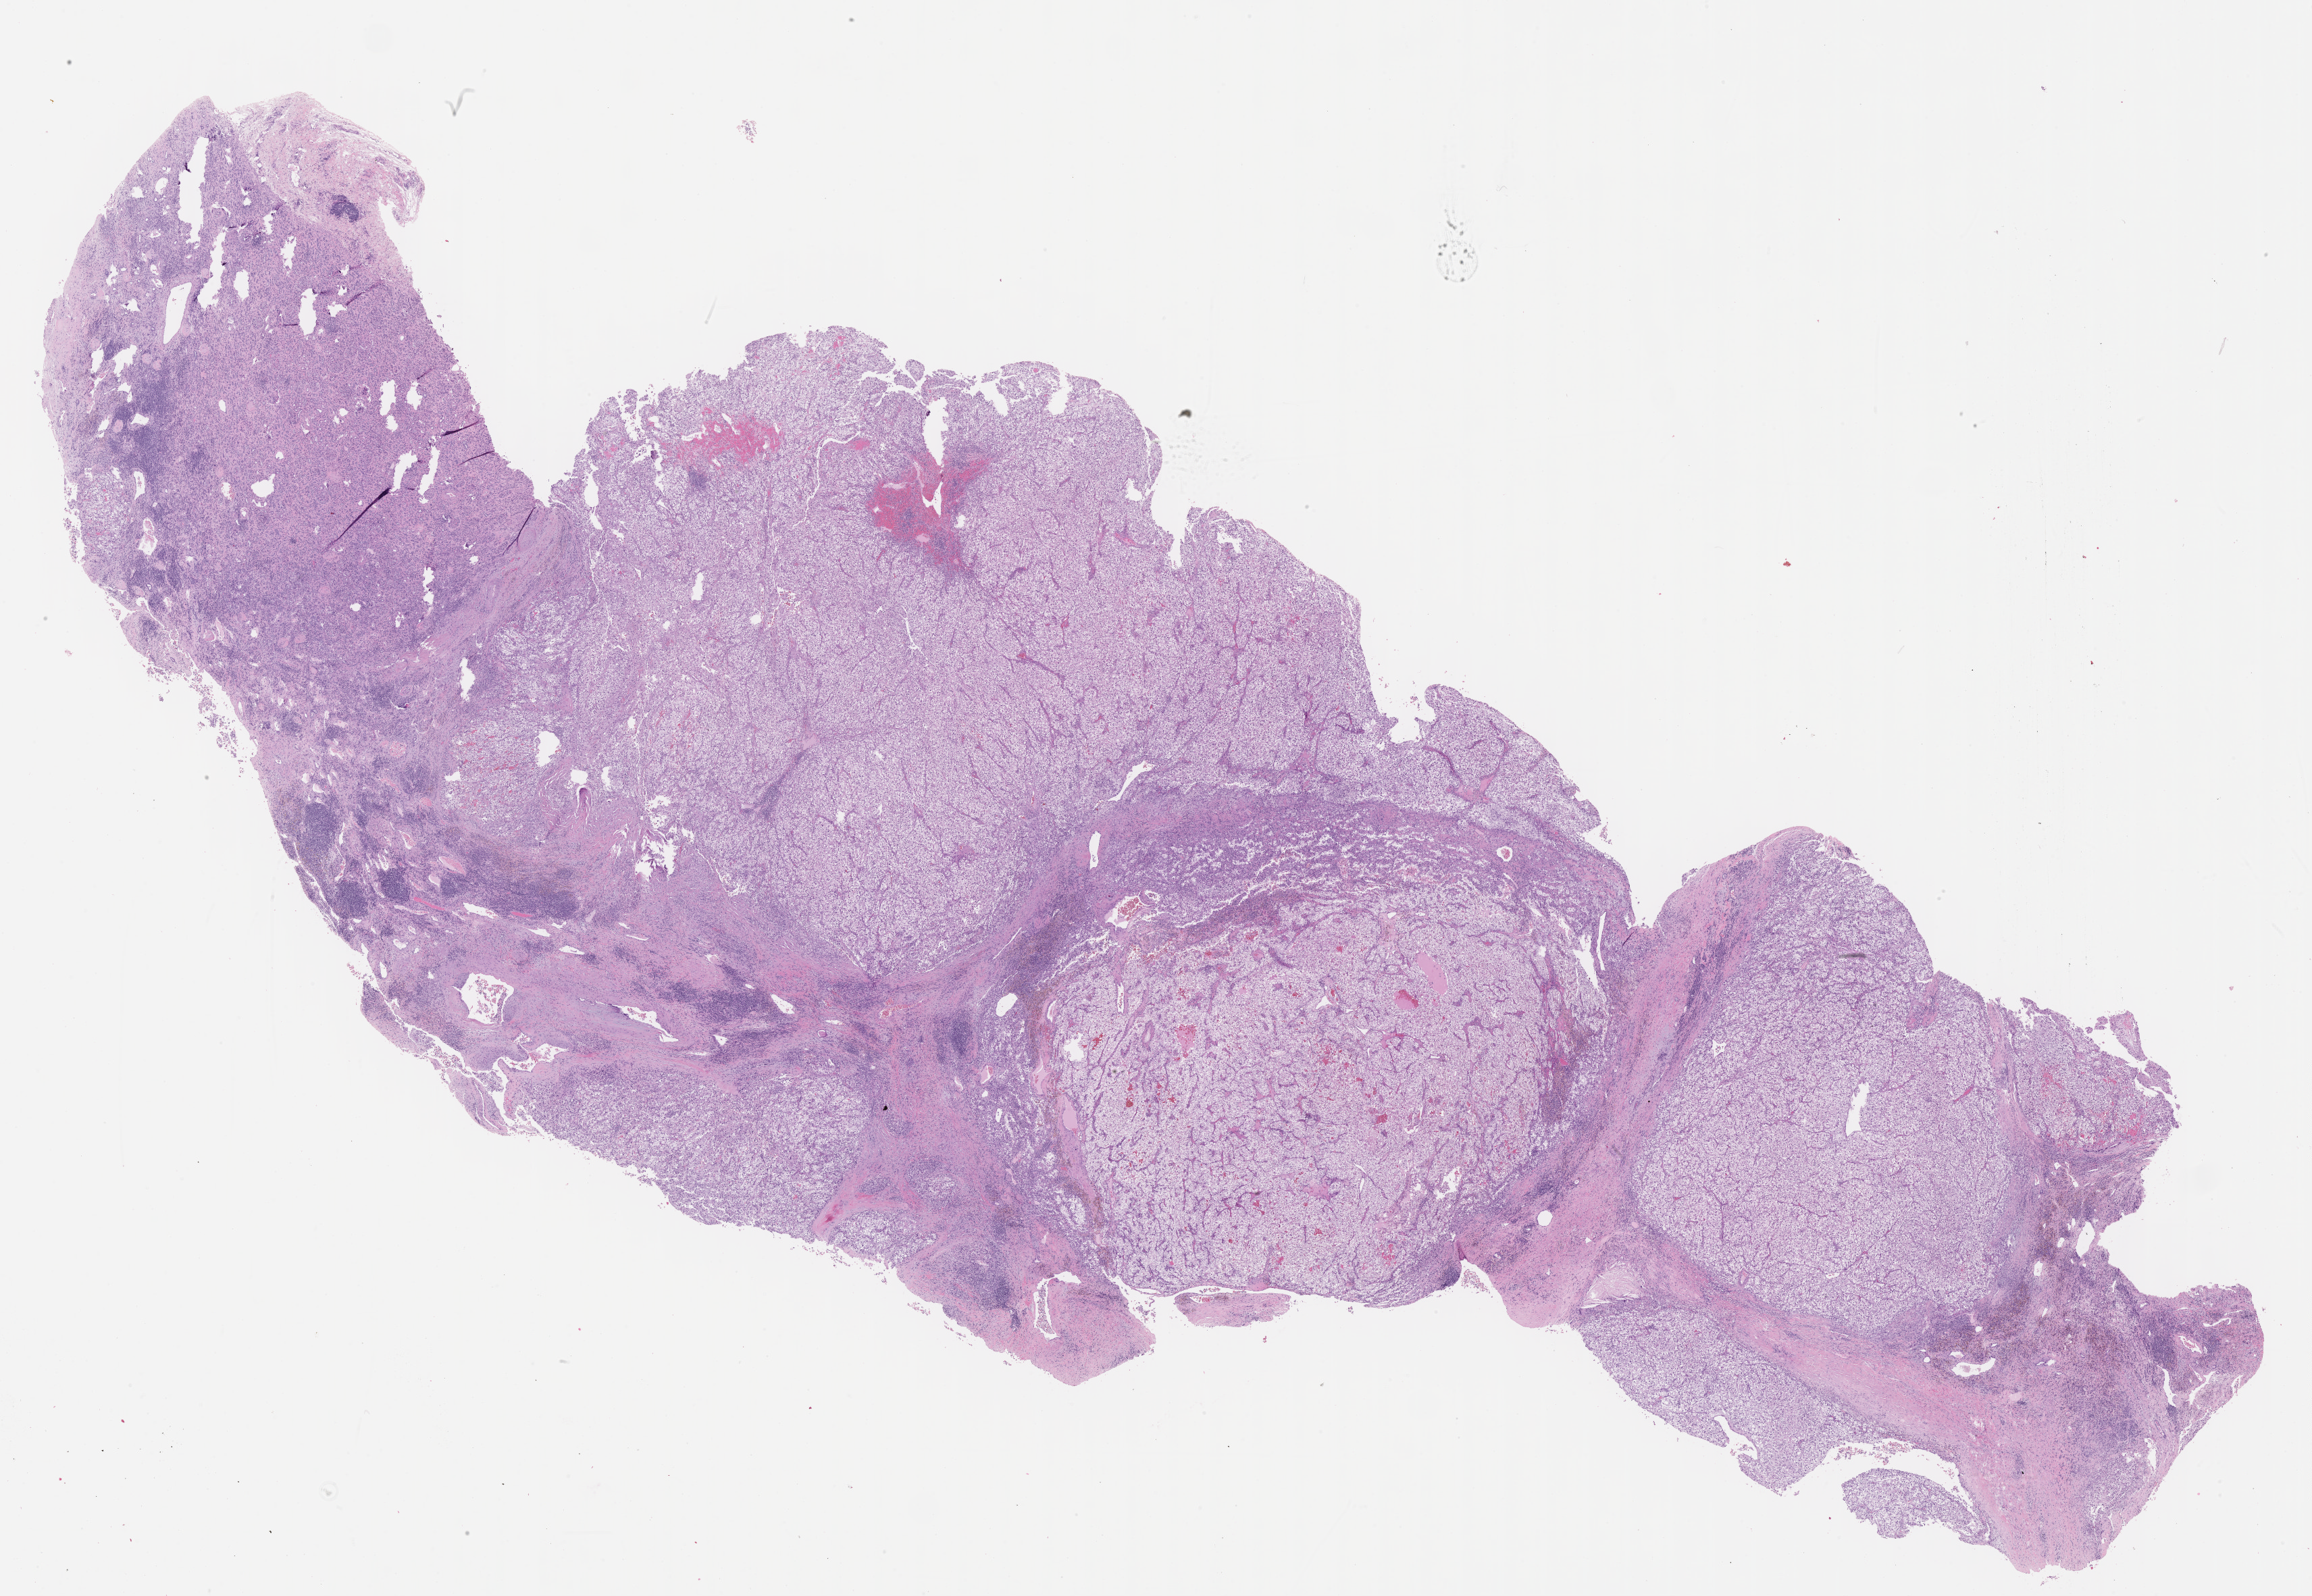
Hematoxylin and eosin (H&E) stained whole-slide image, low-resolution overview of the scanned area, about 27.7 x 19.1 mm. Formalin-fixed paraffin-embedded (FFPE) diagnostic section. Kidney, primary tumour sample. Patient sex: female. Histologic grade: G3 (poorly differentiated).
- laterality: right
- histologic diagnosis: Clear cell adenocarcinoma, NOS
- AJCC pathologic stage: III
- lymph nodes positive (case pathology): 0 of 3 examined